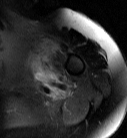
MRI of an extremity soft-tissue mass, one axial slice. Slice 62 of 87 in the series (ordered by position). T2-weighted fat-saturated. MR volume resampled by the dataset authors to the PET/CT grid (not the native acquisition matrix). 3.27 mm slice thickness. 127 × 138 image matrix, field of view 124 × 135 mm. Female patient. Case-level facts recorded for this patient, not image findings: histological type: pleiomorphic leiomyosarcoma; grade: high; site of the primary tumour: left biceps.
Annotated regions visible in this slice (expert contour drawn on MRI and transferred to this co-registered scan by the dataset authors):
- gross tumour volume including surrounding oedema: bounding box (x1, y1, x2, y2) in pixels: (29, 39, 57, 85)
- gross tumour volume (mass): (38, 50, 53, 65)